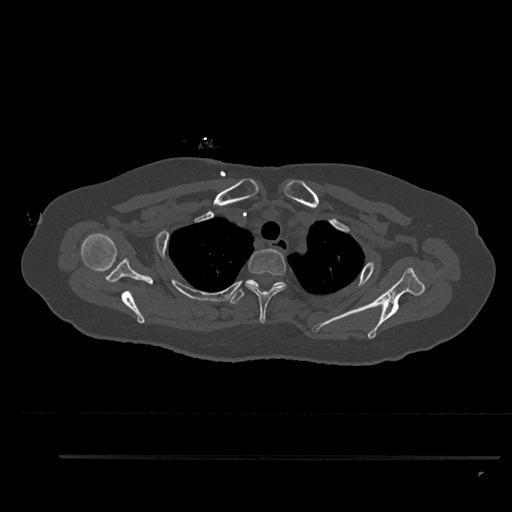
CT including the spine, one axial slice. Position 709 of 797 along the scan axis. 120 kVp. Bone window (W 1800 / L 400 HU). 0.5 mm slice thickness. 512 × 512 image matrix, field of view 408 × 408 mm. Patient: female, 44 years. Case-level facts recorded for this patient, not image findings: primary cancer: renal; vertebrae with lytic lesions (as recorded): L1.
Outlined on this slice (semi-automatically segmented with operator editing):
- T1 vertebra: box from (x=277, y=283) to (x=286, y=287) px
- T2 vertebra: (x=245, y=248)–(x=287, y=323)
- T3 vertebra: (x=230, y=279)–(x=284, y=304)